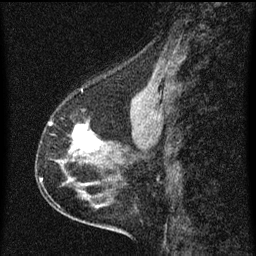
Breast MRI (dynamic contrast-enhanced), one sagittal slice; dynamic contrast-enhanced series, image 2 of 3 at this slice position (ordered by acquisition); 1.5 T; TE 4.2 ms, TR 8 ms; 2 mm slice thickness; 256 × 256 image matrix, field of view 180 × 180 mm. Female patient, age 56 years.
Structures marked on this image (semi-automatic segmentation, software-assisted and operator-edited):
- analysis volume of interest (the breast-tissue region the enhancement analysis was run in; not a lesion): bounding box [x1, y1, x2, y2] px = [49, 114, 102, 181]
- tumour enhancement mask (voxels above the 70 % enhancement threshold inside the analysis volume of interest): [73, 125, 96, 149]